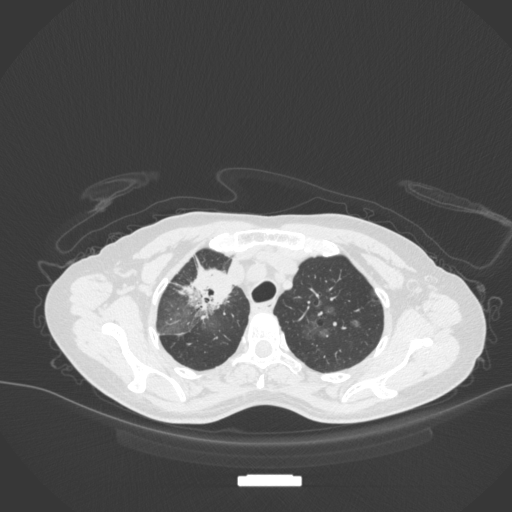
Chest CT, one axial slice; slice 262 of 311 in the series (ordered by position); 120 kVp; lung window (W 1500 / L -600 HU); 512 × 512 image matrix, field of view 400 × 400 mm. Female patient, age 59 years. Case-level facts recorded for this patient, not image findings: clinical TNM (as recorded): T3 N0 M0.
Structures marked on this image (bounding box drawn by a radiologist):
- lung tumour (recorded histology: adenocarcinoma): box from (x=178, y=262) to (x=243, y=327) px